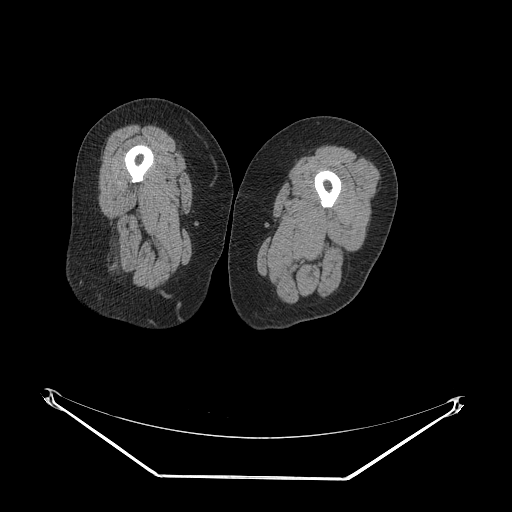
CT of an extremity soft-tissue mass (from a PET/CT study), one axial slice. Slice 19 of 257 in the series (ordered by position). 140 kVp. Soft-tissue window (W 400 / L 40 HU). 512 × 512 image matrix, field of view 500 × 500 mm. Female patient. Case-level facts recorded for this patient, not image findings: histological type: synovial sarcoma; grade: intermediate; site of the primary tumour: right buttock.
Structures marked on this image (expert contour drawn on MRI and transferred to this co-registered scan by the dataset authors):
- gross tumour volume including surrounding oedema: bounding box <98,254,113,275> (left, top, right, bottom; pixels)